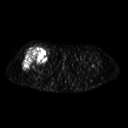
FDG PET of an extremity soft-tissue mass (from a PET/CT study), one axial slice. Position 265 of 311 along the scan axis. 3.27 mm slice thickness. 128 × 128 image matrix, field of view 500 × 500 mm. Patient: female, 57 years. From the clinical record (not read from this slice): histological type: pleiomorphic undifferentiated sarcoma; grade: high; site of the primary tumour: right quadricep.
Annotated regions visible in this slice (expert contour drawn on MRI and transferred to this co-registered scan by the dataset authors):
- tumour plus oedema (research contour): bounding box (x1, y1, x2, y2) in pixels: (22, 47, 48, 70)
- tumour (research contour): (22, 47, 48, 70)